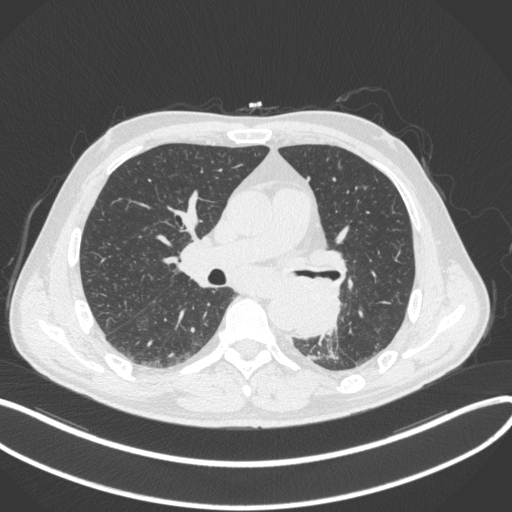
Chest CT, one axial slice. Position 189 of 328 along the scan axis. Lung window (W 1500 / L -600 HU). 1 mm slice thickness. 512 × 512 image matrix, field of view 400 × 400 mm. Patient: male, 59 years. Case-level facts recorded for this patient, not image findings: clinical TNM (as recorded): T2a N2 M0.
Annotated regions visible in this slice (bounding box drawn by a radiologist):
- lung tumour (recorded histology: squamous cell carcinoma): bounding box [x1, y1, x2, y2] px = [291, 281, 344, 342]